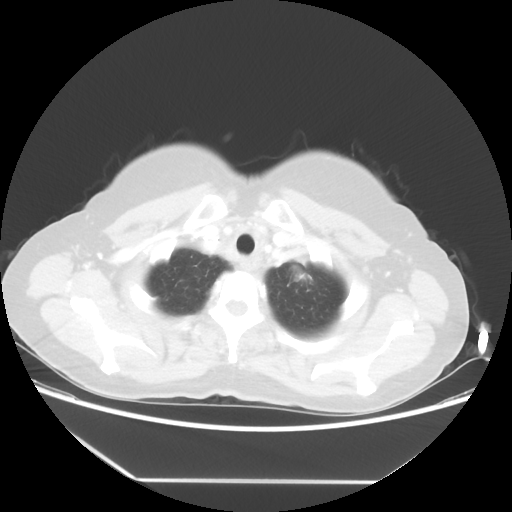
Chest CT, one axial slice; slice 47 of 52 in the series (ordered by position); 100 kVp; lung window (W 1500 / L -600 HU); 512 × 512 image matrix, field of view 390 × 390 mm. Female patient, age 50 years. From the clinical record (not read from this slice): clinical TNM (as recorded): T2 N3 M0.
Outlined on this slice (bounding box drawn by a radiologist):
- lung tumour (recorded histology: adenocarcinoma): bounding box [x1, y1, x2, y2] px = [275, 249, 322, 299]